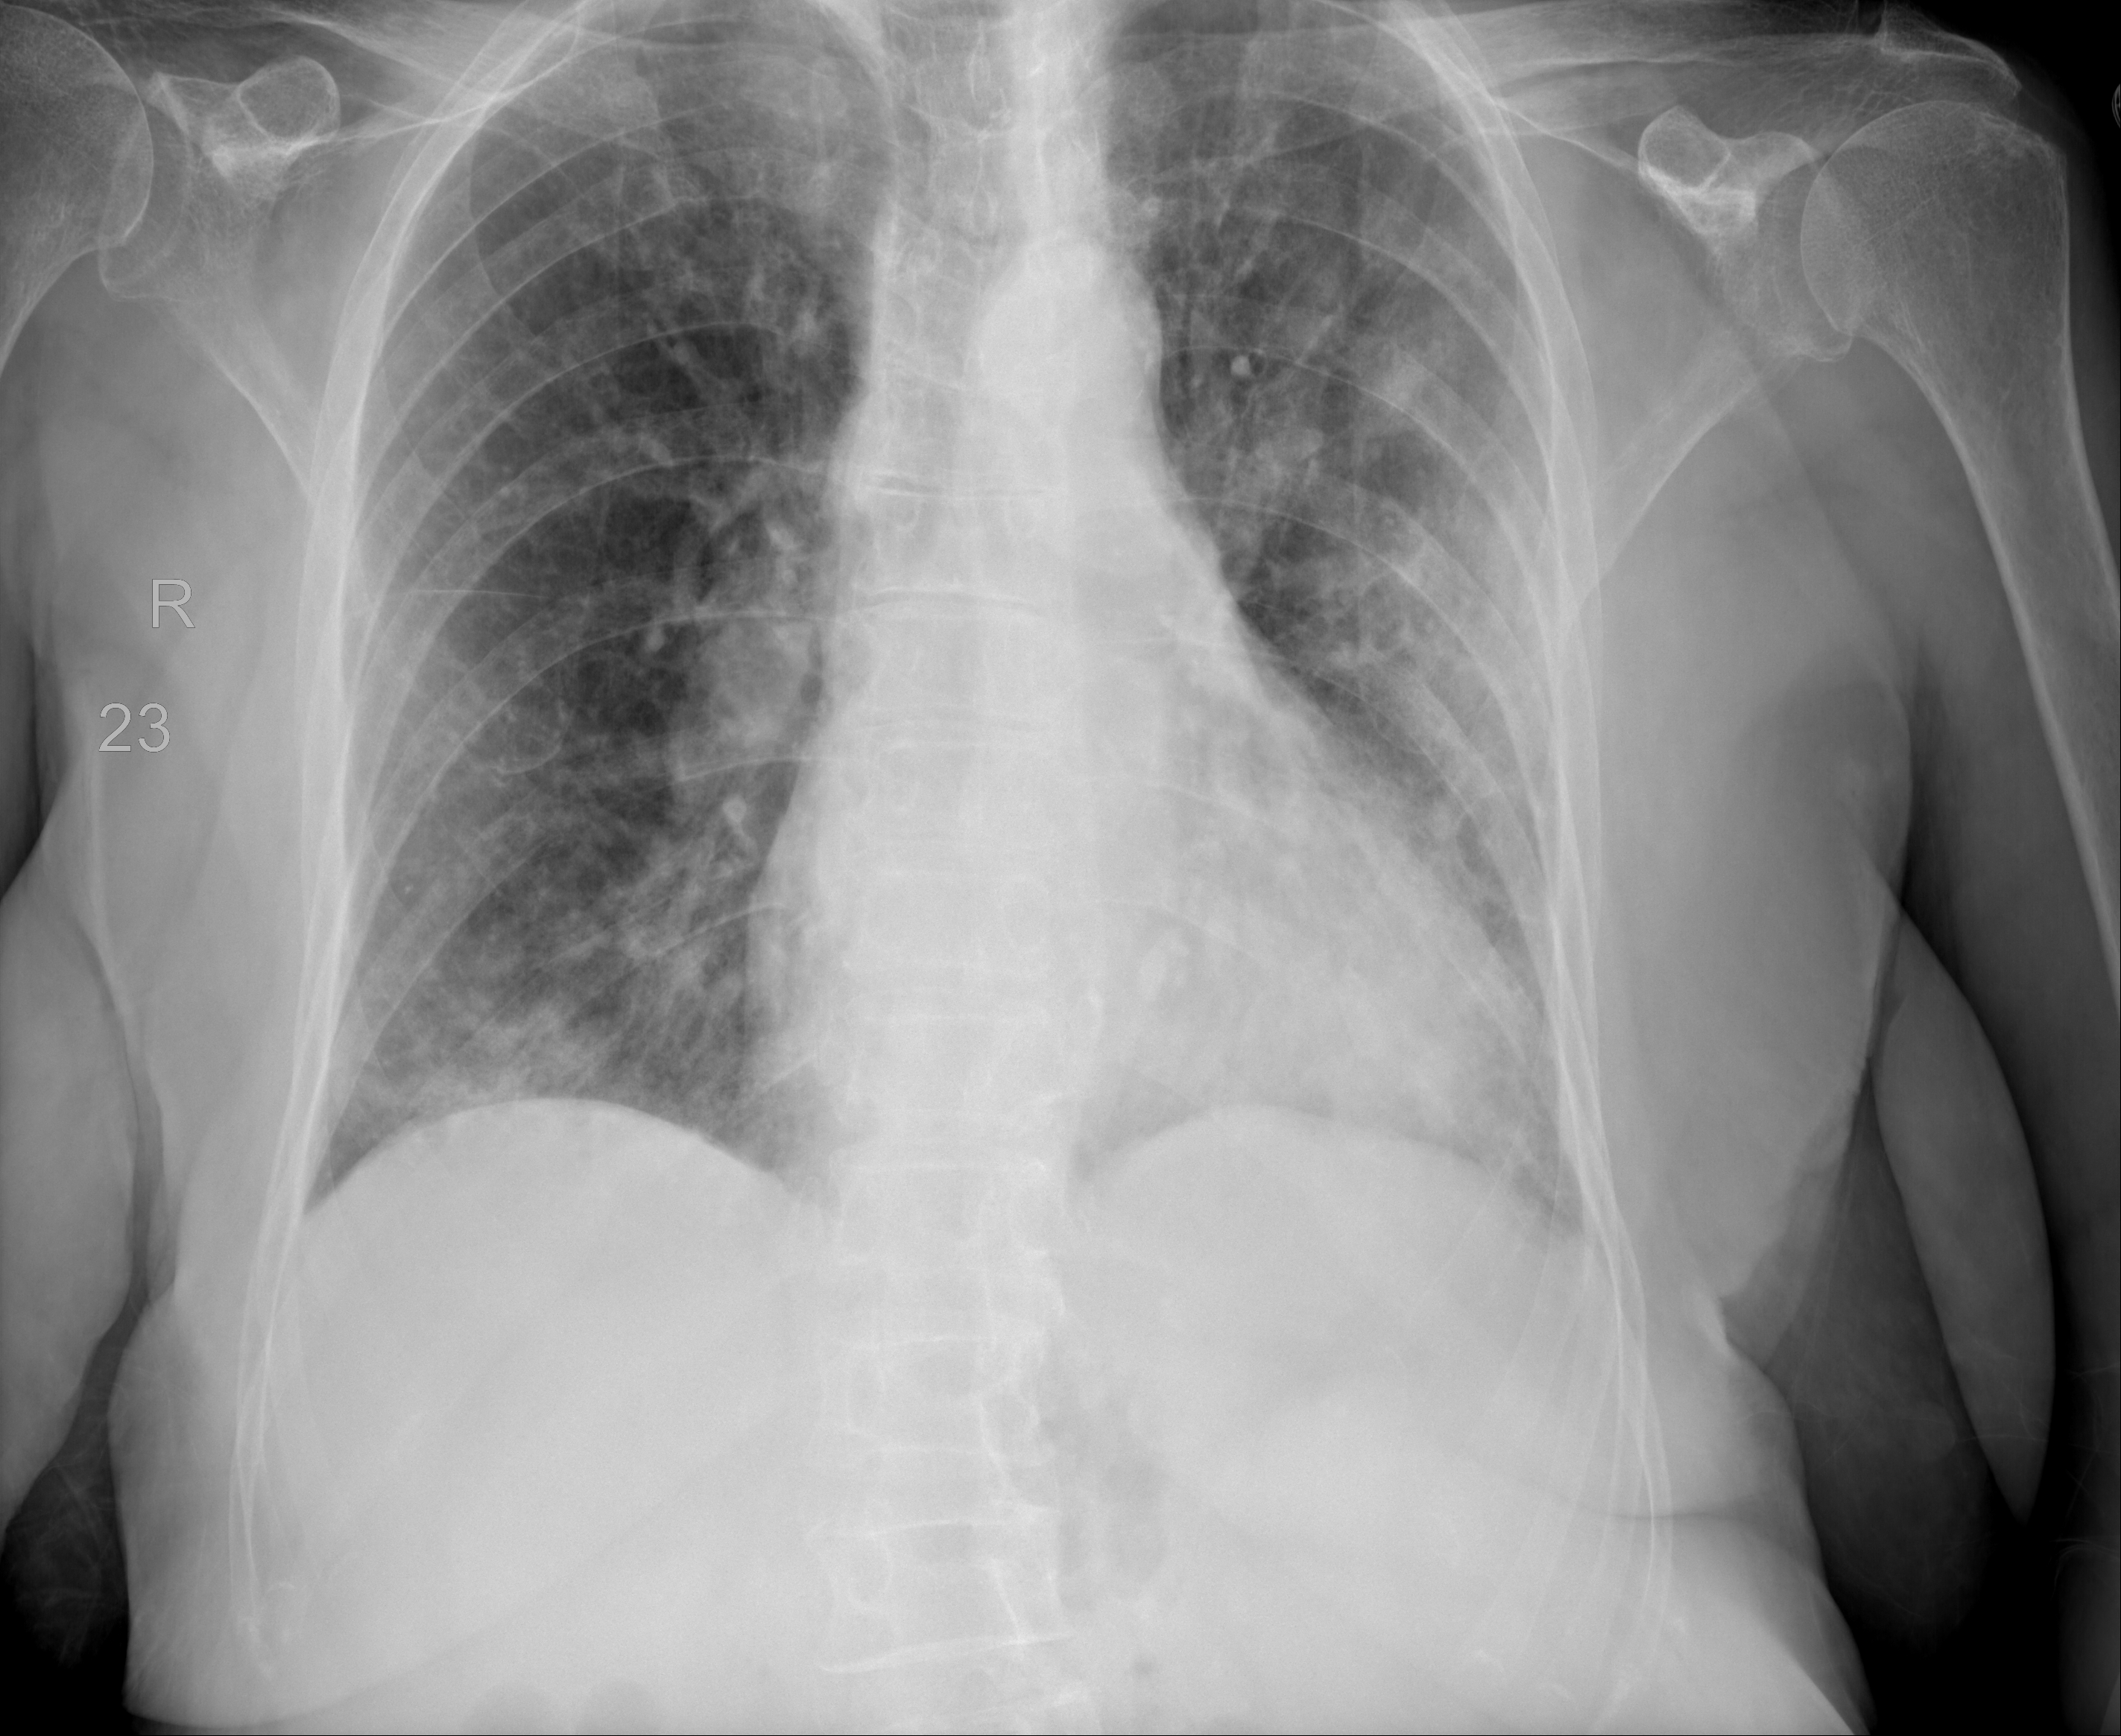
Chest radiograph, PA projection. Female patient, age 75 years; COVID-19 (test-positive).
Key findings recorded by the radiologist: Patchy ground-glass changes are seen within the left lung and in the right lower lung not significantly changed compared to the prior study.